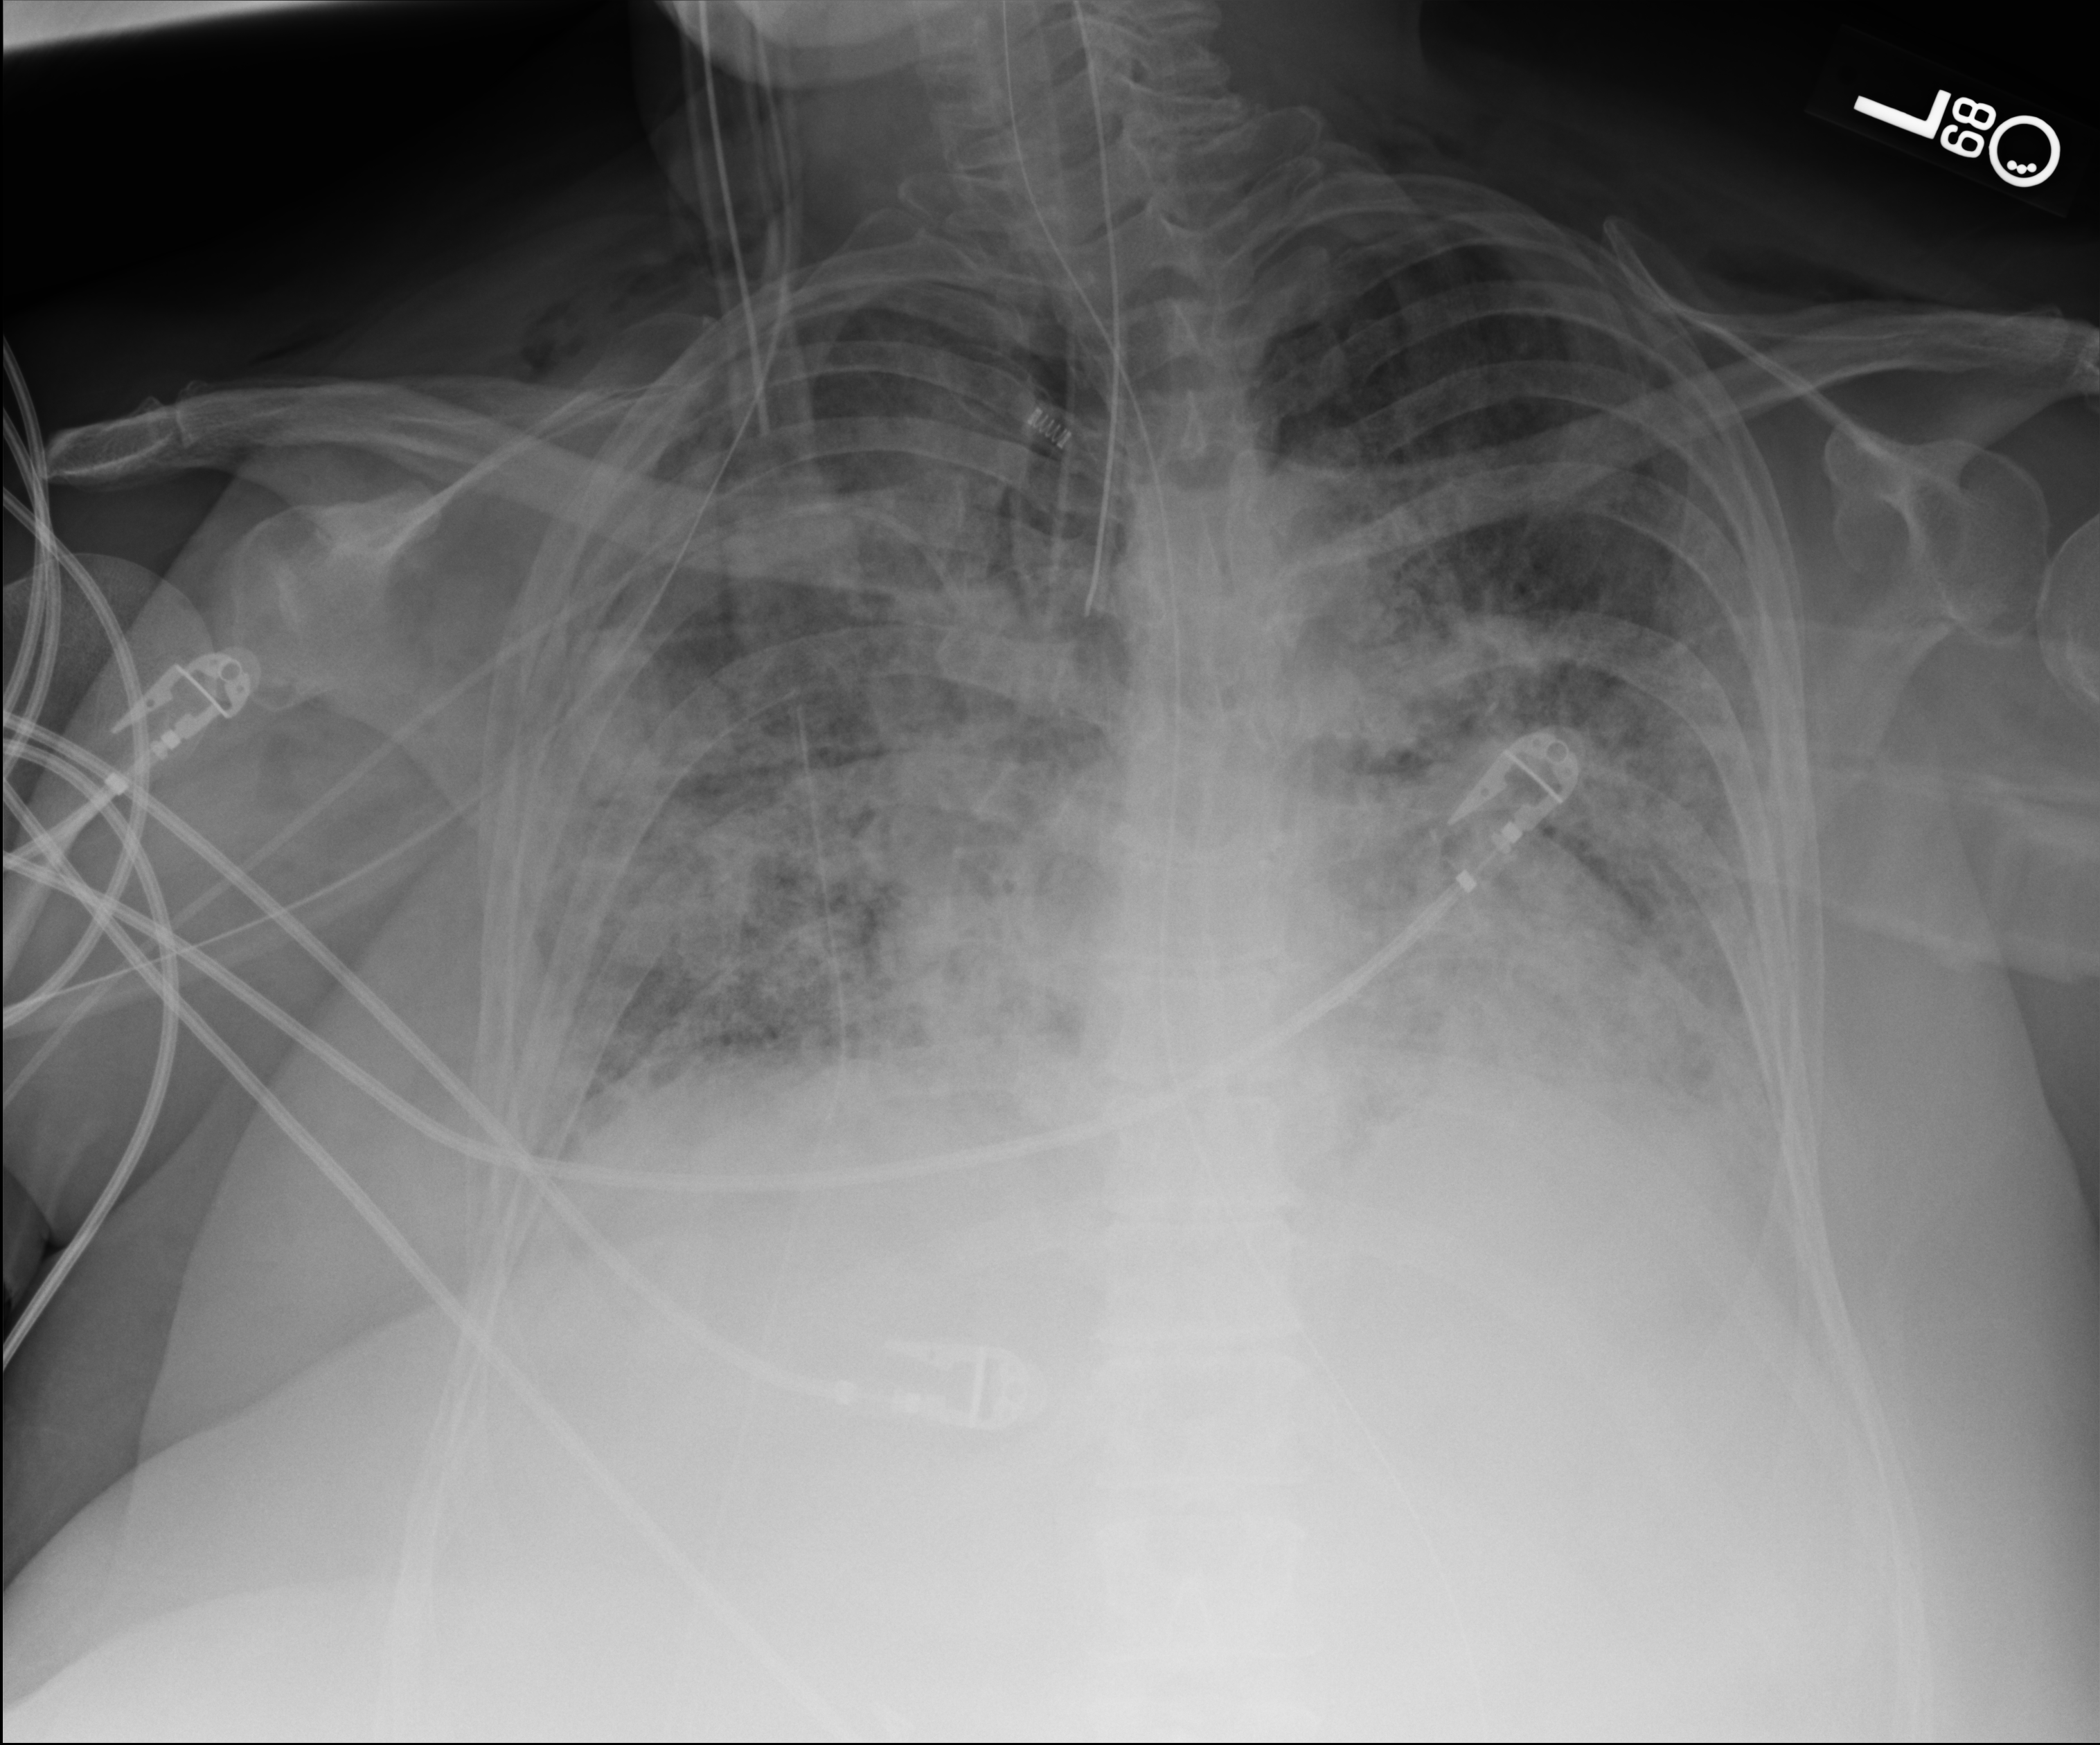
Portable chest radiograph. Female patient hospitalised with COVID-19, age 60–74 years.
From the hospital-stay record, not from the radiograph (when in the stay this image was taken is not recorded):
- smoking status (admission record): never
- COPD (admission record): no